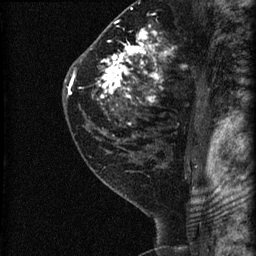
Breast MRI (dynamic contrast-enhanced), one sagittal slice. Slice 45 of 60 in the series (ordered by position). Dynamic contrast-enhanced series, image 2 of 3 at this slice position (ordered by acquisition). 1.5 T. TE 4.2 ms, TR 22.7 ms. 256 × 256 image matrix, field of view 180 × 180 mm. Patient: female, 45 years. Case-level facts recorded for this patient, not image findings: setting: breast cancer imaged before/during neoadjuvant chemotherapy; receptor status: HR-positive, HER2-negative.
Structures marked on this image (semi-automatically segmented with operator editing):
- analysis volume of interest (the breast-tissue region the enhancement analysis was run in; not a lesion): box from (x=74, y=11) to (x=205, y=140) px
- tumour enhancement mask (voxels above the 90 % enhancement threshold inside the analysis volume of interest): (x=74, y=25)–(x=171, y=124)